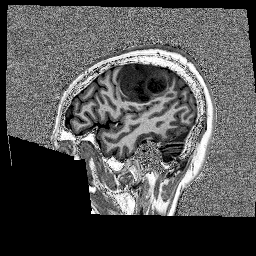
Brain MRI from a brain-tumour surgery series, one sagittal slice. Slice 42 of 176 in the series (ordered by position). 1 mm slice thickness. 256 × 256 image matrix, field of view 256 × 256 mm. Case-level facts recorded for this patient, not image findings: histopathology: Glioblastoma; WHO grade: 4.
Annotated regions visible in this slice (outlined manually by an expert reader):
- tumour: box from (x=118, y=62) to (x=175, y=102) px